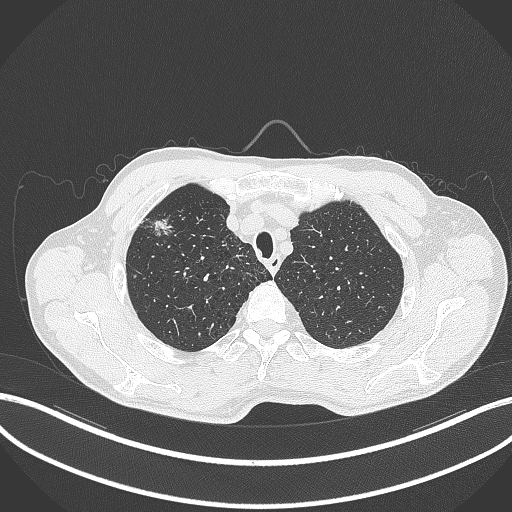
Chest CT, one axial slice. Position 353 of 427 along the scan axis. 120 kVp. Lung window (W 1500 / L -600 HU). 1 mm slice thickness. 512 × 512 image matrix, field of view 400 × 400 mm. Patient: male, 69 years. Case-level facts recorded for this patient, not image findings: clinical TNM (as recorded): T1b N1 M0.
Structures marked on this image (rectangle marked by the reading radiologist):
- lung tumour (recorded histology: adenocarcinoma): box from (x=140, y=211) to (x=174, y=241) px